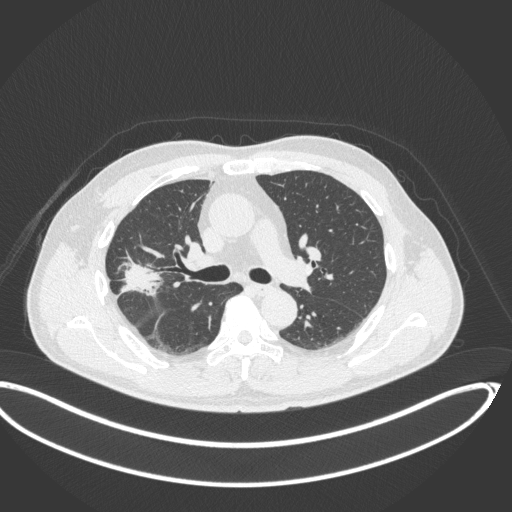
Chest CT, one axial slice; slice 211 of 341 in the series (ordered by position); 120 kVp; lung window (W 1500 / L -600 HU); 1 mm slice thickness; 512 × 512 image matrix. Male patient, age 63 years. From the clinical record (not read from this slice): clinical TNM (as recorded): T1c N0 M0; histopathological grade: G2-3.
Outlined on this slice (bounding box drawn by a radiologist):
- lung tumour (recorded histology: adenocarcinoma): box from (x=116, y=254) to (x=167, y=303) px